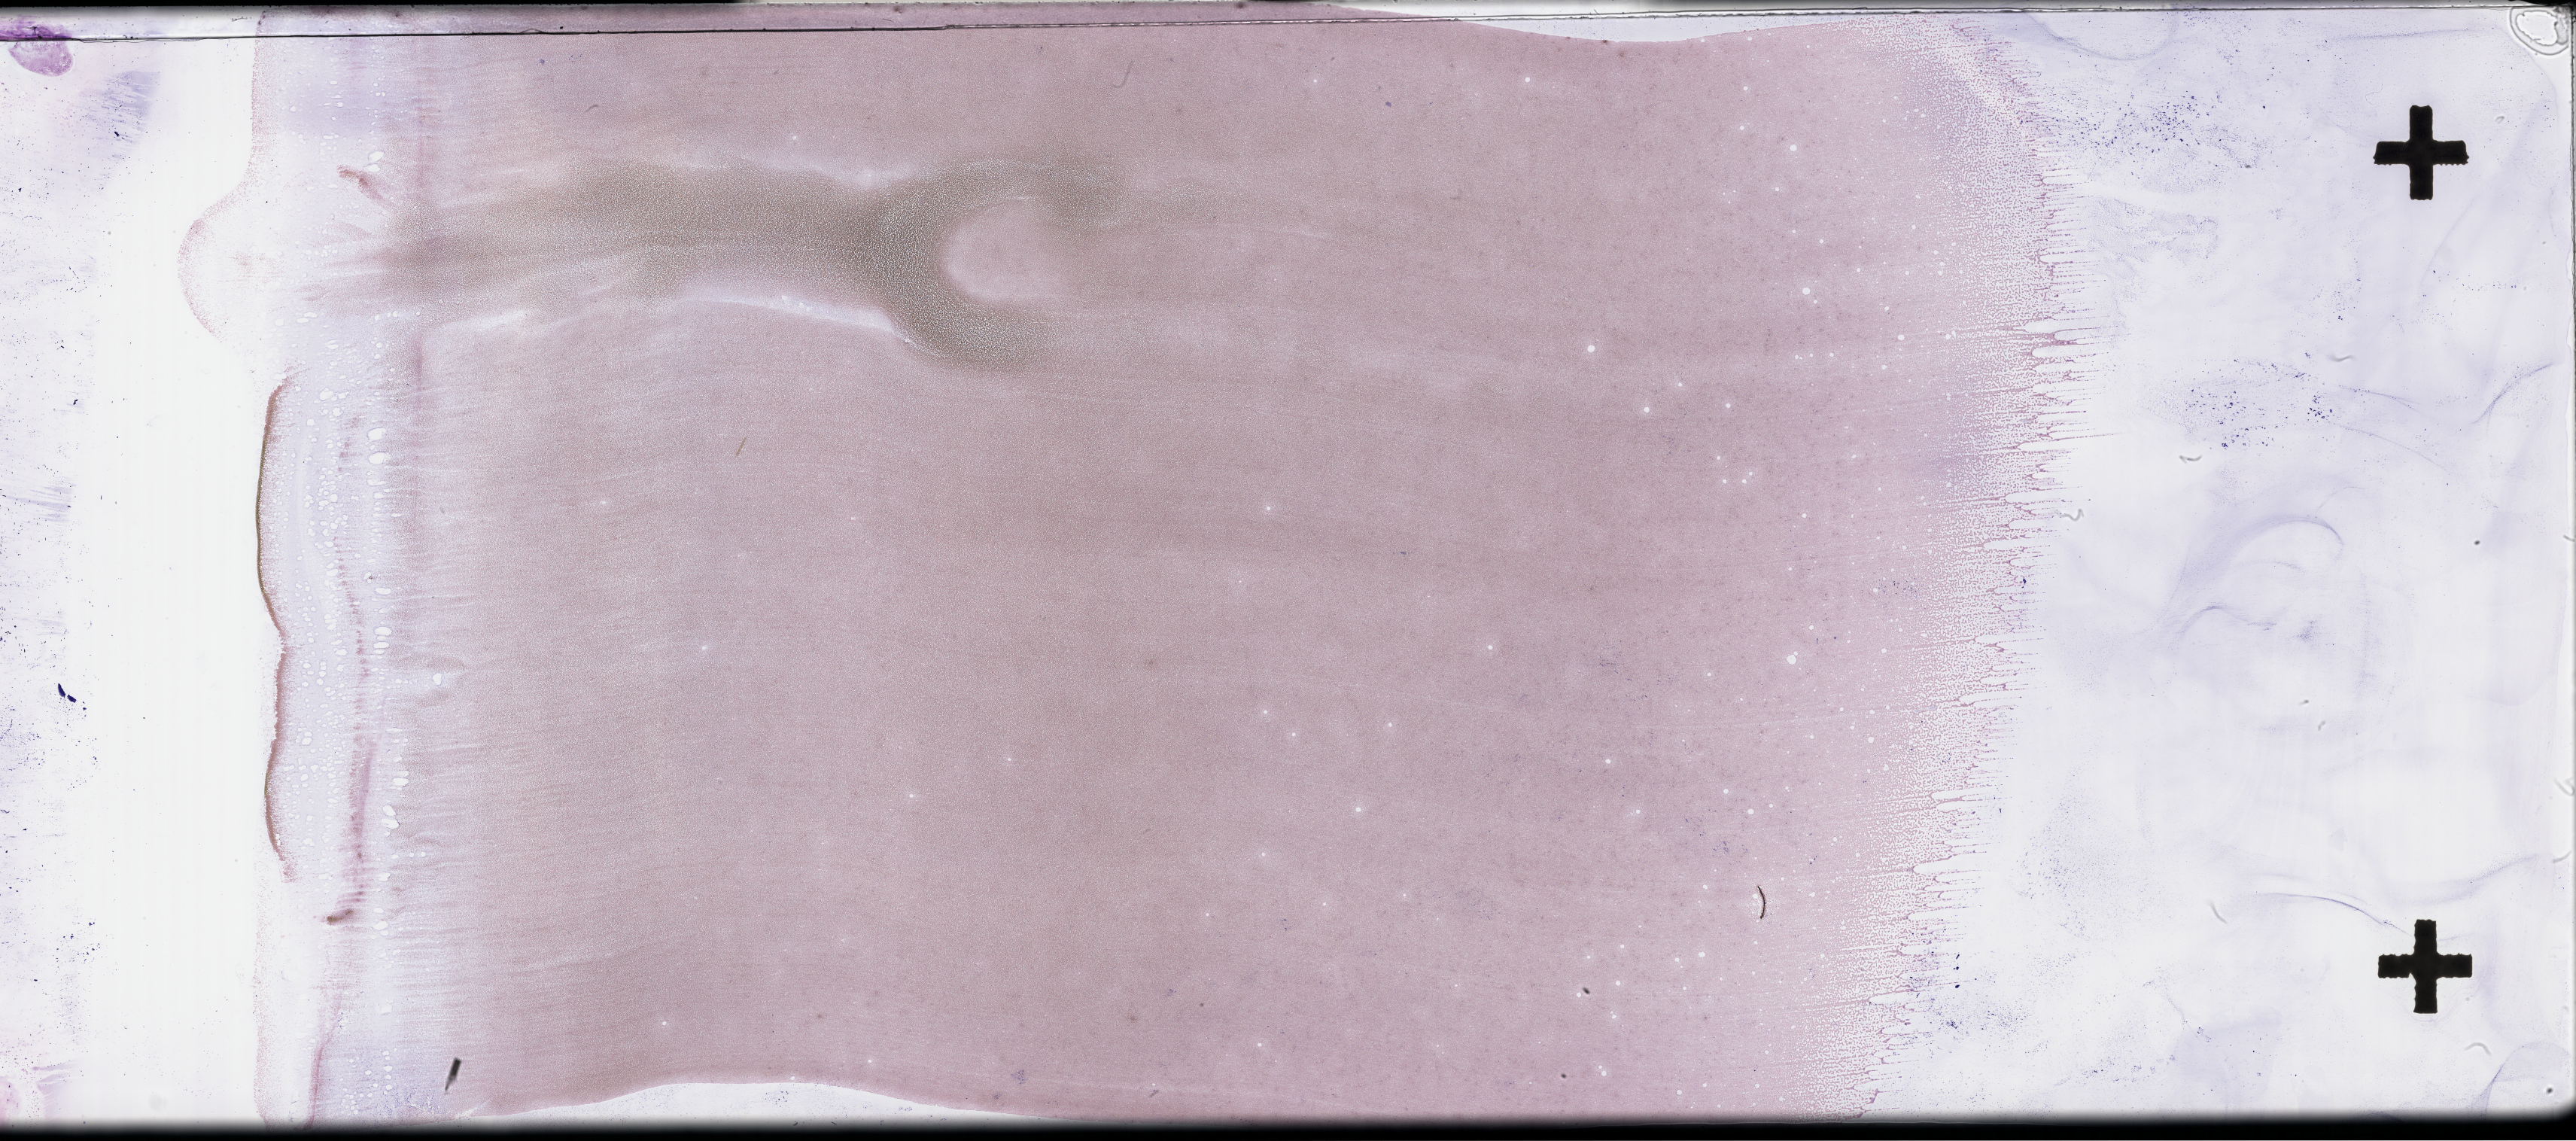
Wright-Giemsa-stained whole blood smear, whole-slide image, whole scanned area (about 55.3 x 24.5 mm) shown as a low-resolution overview, EDTA-anticoagulated smear. Patient: female.
* patient diagnosis: Plasma Cell Myeloma